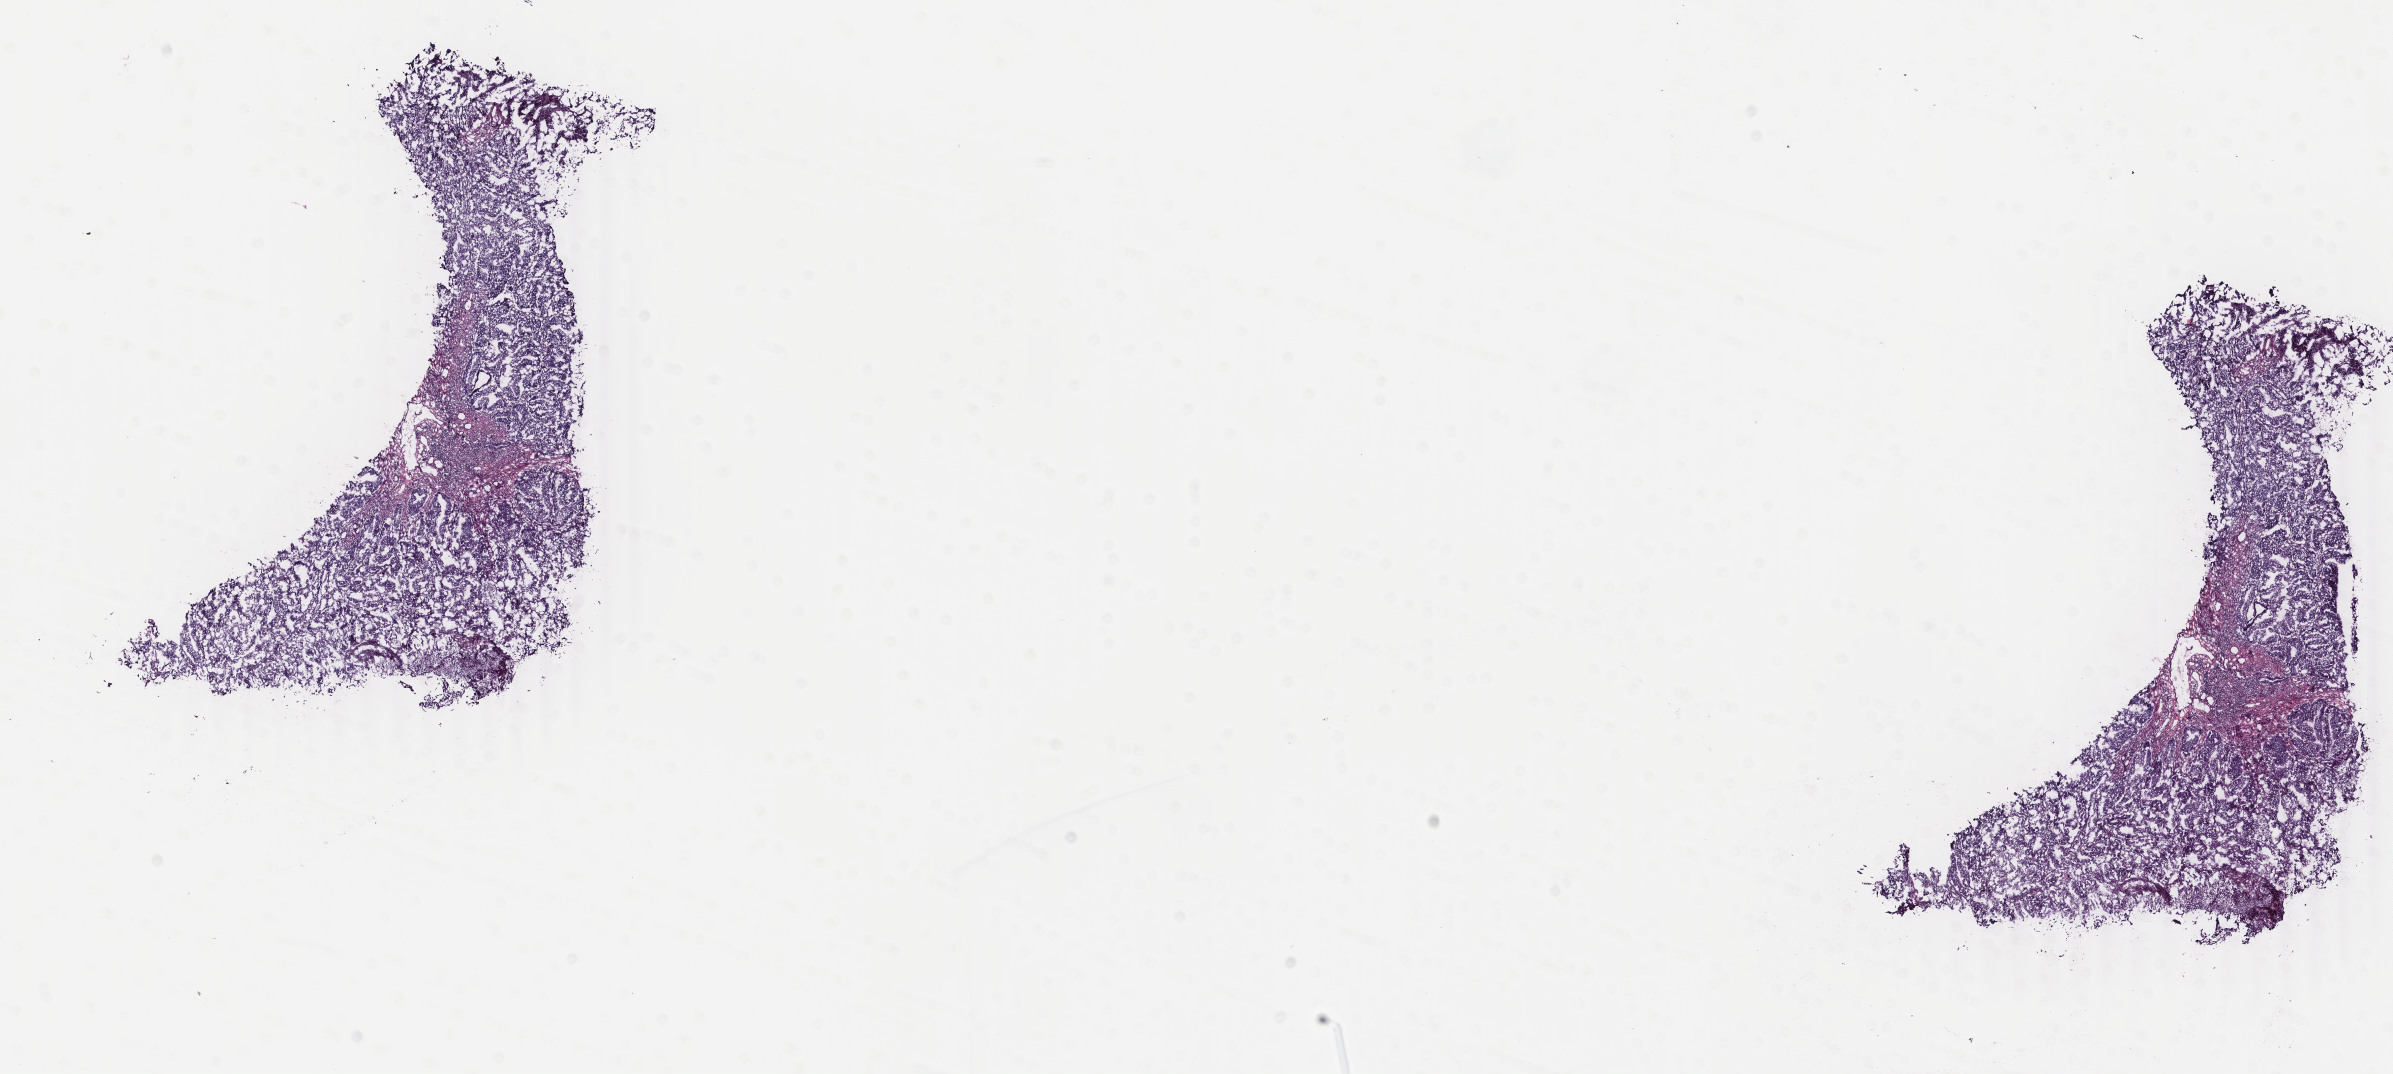
Digitized H&E-stained tissue section (whole slide), low-resolution overview of the scanned area, about 19.0 x 8.5 mm (from a 40x scan). Frozen section. Primary tumour sample from the uterus. Female, age 48 years at initial diagnosis. Histologic grade: G1 (well differentiated). Slide review estimates, as recorded: tumour cells 60%, tumour nuclei 80%, normal cells 20%, stromal cells 0%, necrosis 20%. Infiltration values recorded for this section: lymphocyte infiltration 10%, monocyte infiltration 0%, neutrophil infiltration 10%.
Lymph nodes positive (case pathology): 0 of 26 examined. Pathologic diagnosis: Endometrioid adenocarcinoma, NOS (endometrium). FIGO stage: IB.